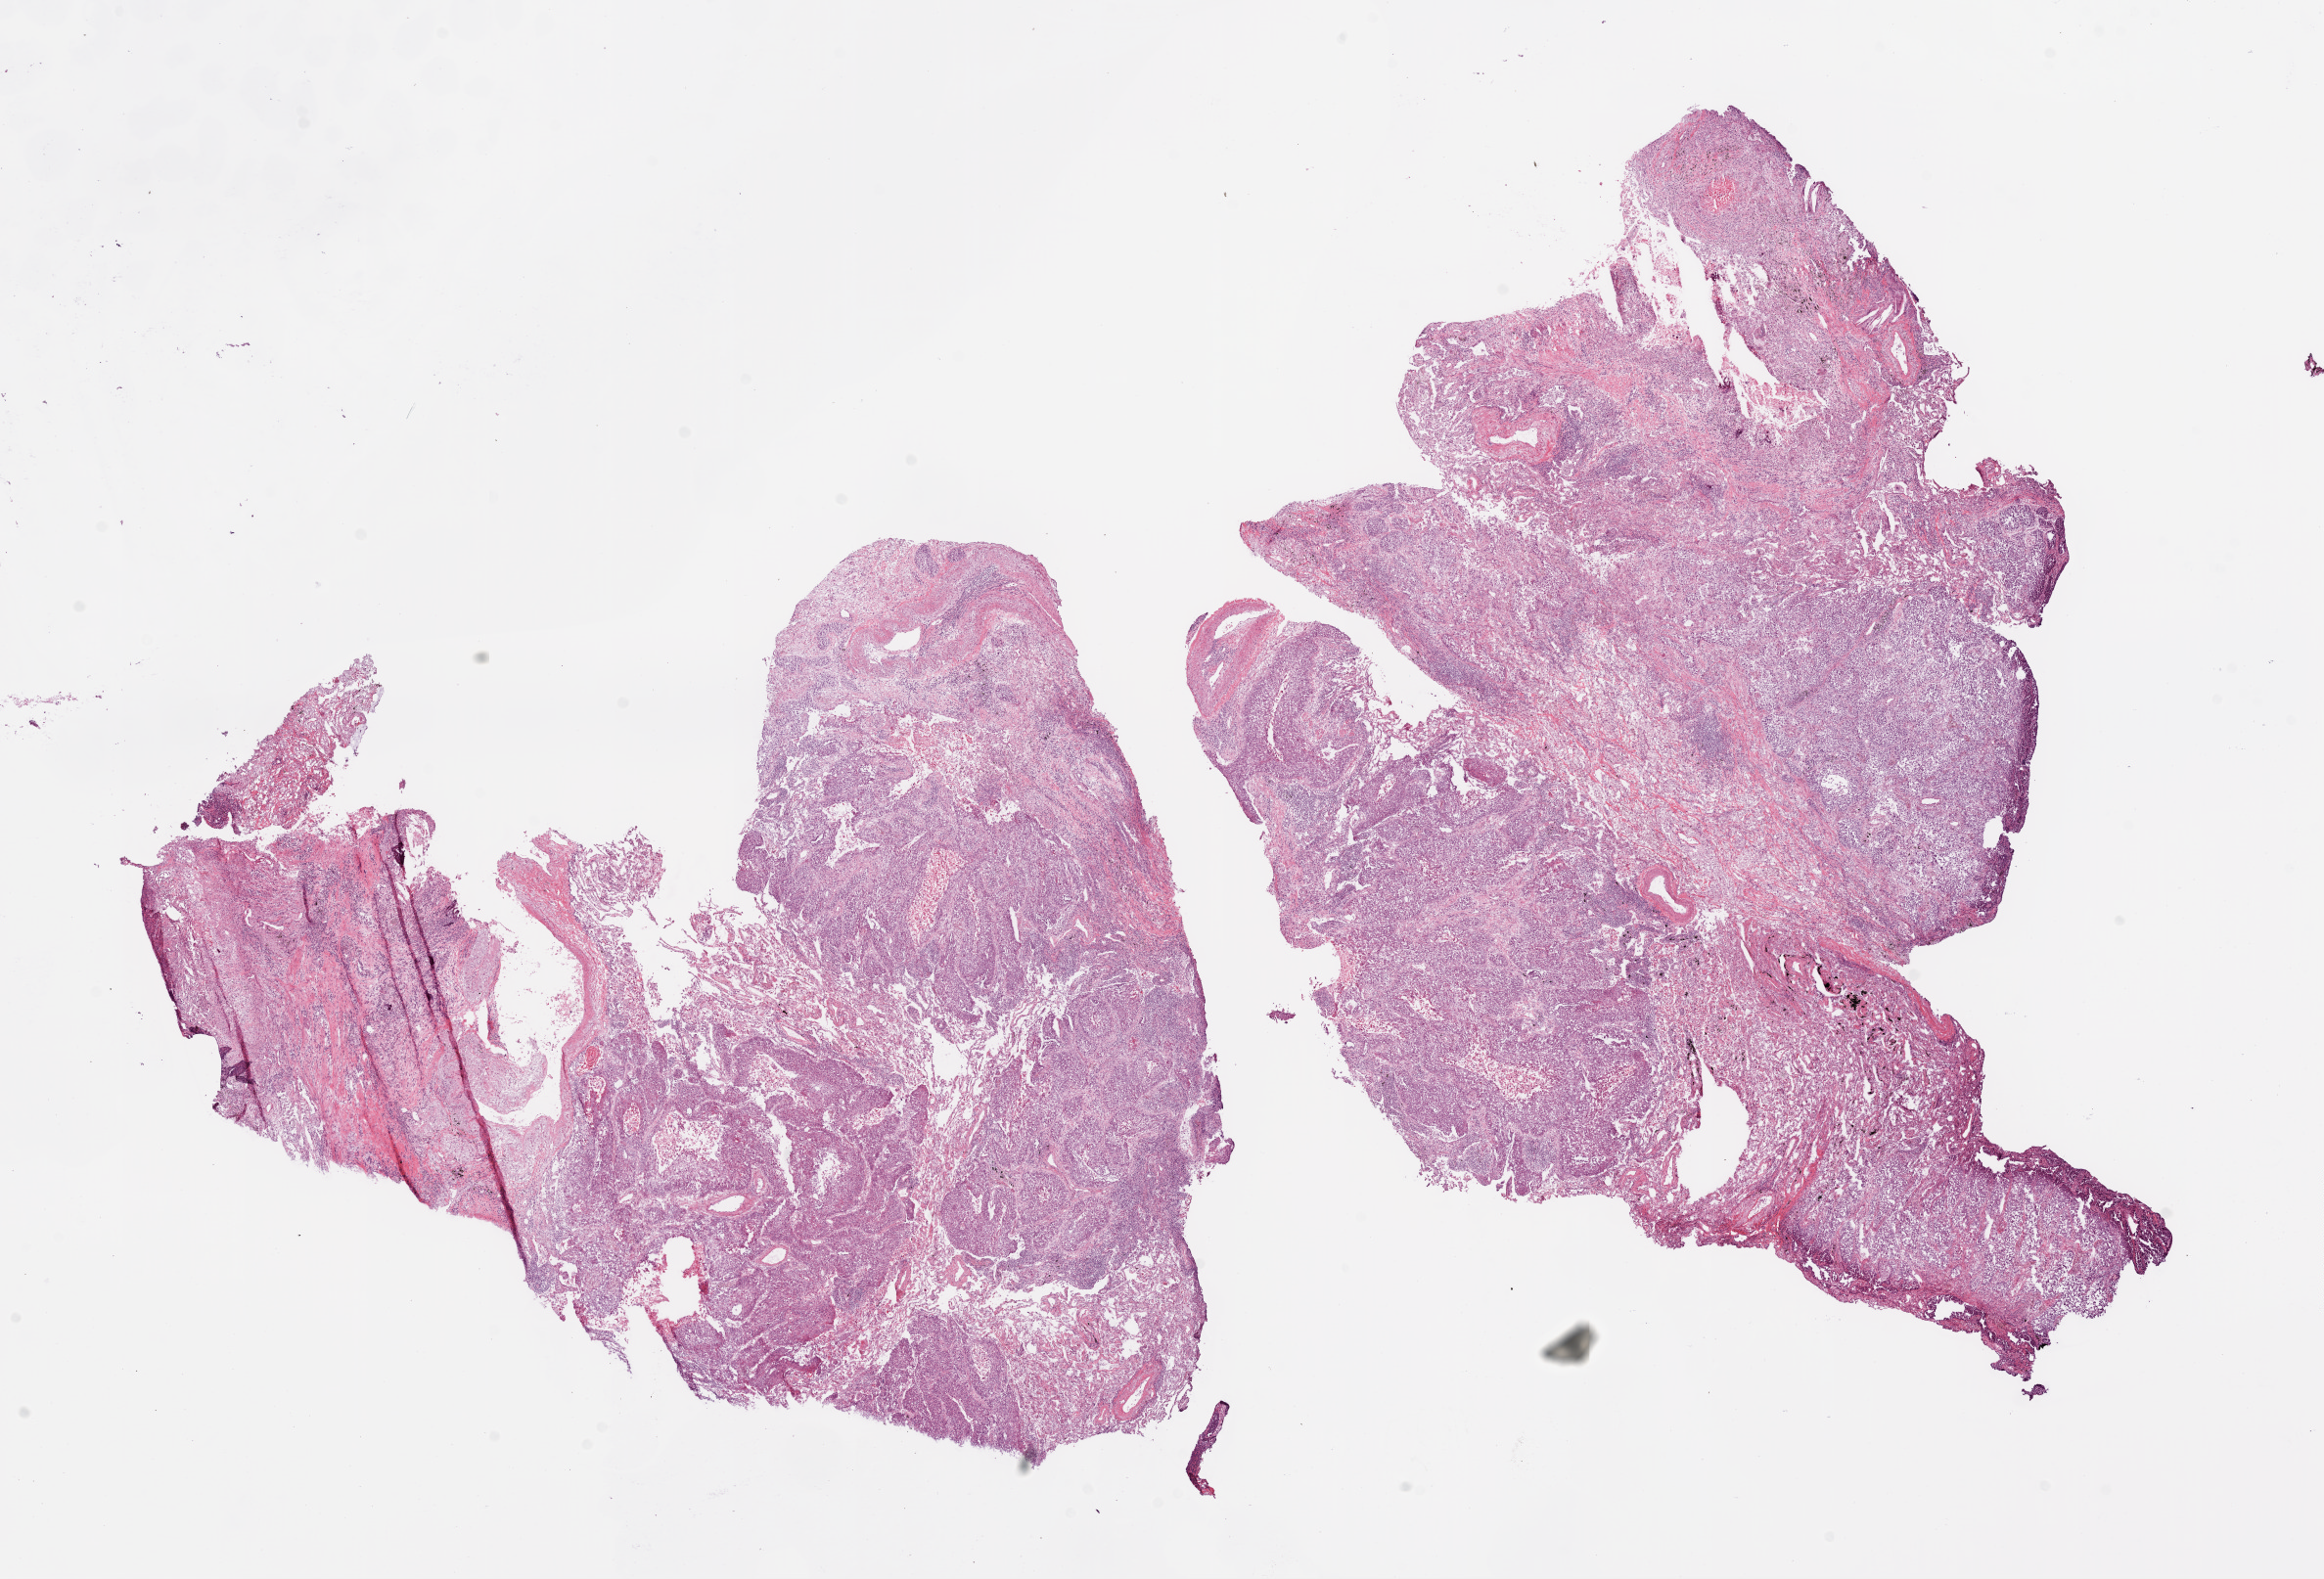
H&E-stained whole-slide image — shown as a low-resolution overview of the whole scanned area (about 19.1 x 13.0 mm, from a 20x scan). Frozen section from the top of the tissue portion. Primary tumour sample from the lung. Male, age 73 years at initial diagnosis. Slide review estimates, as recorded: tumour cells 65%, tumour nuclei 70%, normal cells 10%, stromal cells 20%, necrosis 5%.
Laterality: left. Pathologic diagnosis: Squamous cell carcinoma, NOS (upper lobe, lung). AJCC pathologic stage: IB (6th edition).